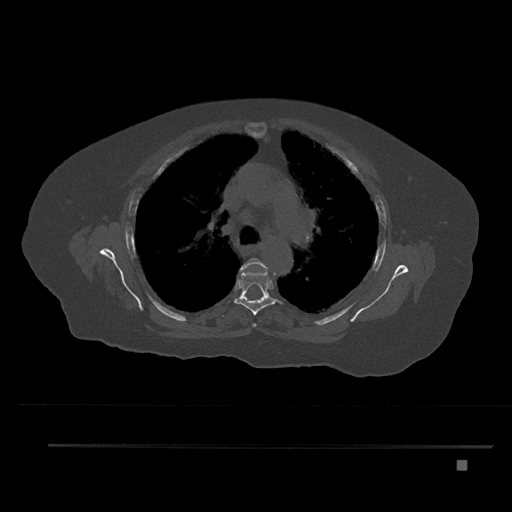
CT including the spine, one axial slice; position 571 of 797 along the scan axis; reconstruction kernel Br40s/3; bone window (W 1800 / L 400 HU); 0.5 mm slice thickness; 512 × 512 image matrix. Female patient, age 76 years. Case-level facts recorded for this patient, not image findings: primary cancer: lung.
Annotated regions visible in this slice (semi-automatically segmented with operator editing):
- T4 vertebra: bounding box (x1, y1, x2, y2) in pixels: (240, 258, 268, 328)
- T5 vertebra: (230, 271, 283, 315)